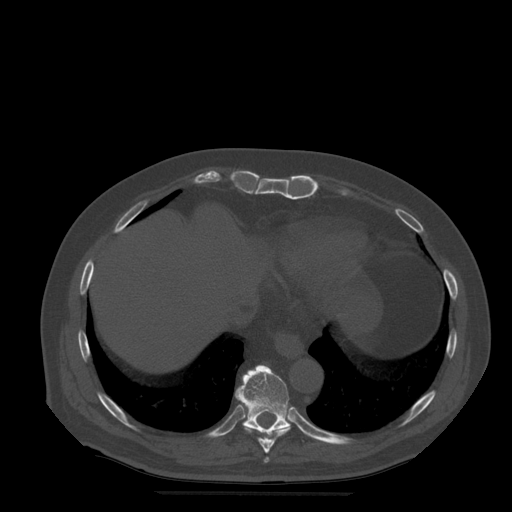
CT including the spine, one axial slice; position 278 of 522 along the scan axis; bone window (W 1800 / L 400 HU); 512 × 512 image matrix, field of view 420 × 420 mm. Patient age 72 years. Case-level facts recorded for this patient, not image findings: primary cancer: prostate.
Structures marked on this image (semi-automatically segmented with operator editing):
- T10 vertebra: bounding box [x1, y1, x2, y2] px = [235, 365, 291, 435]
- T8 vertebra: [264, 457, 269, 463]
- T9 vertebra: [244, 426, 291, 454]